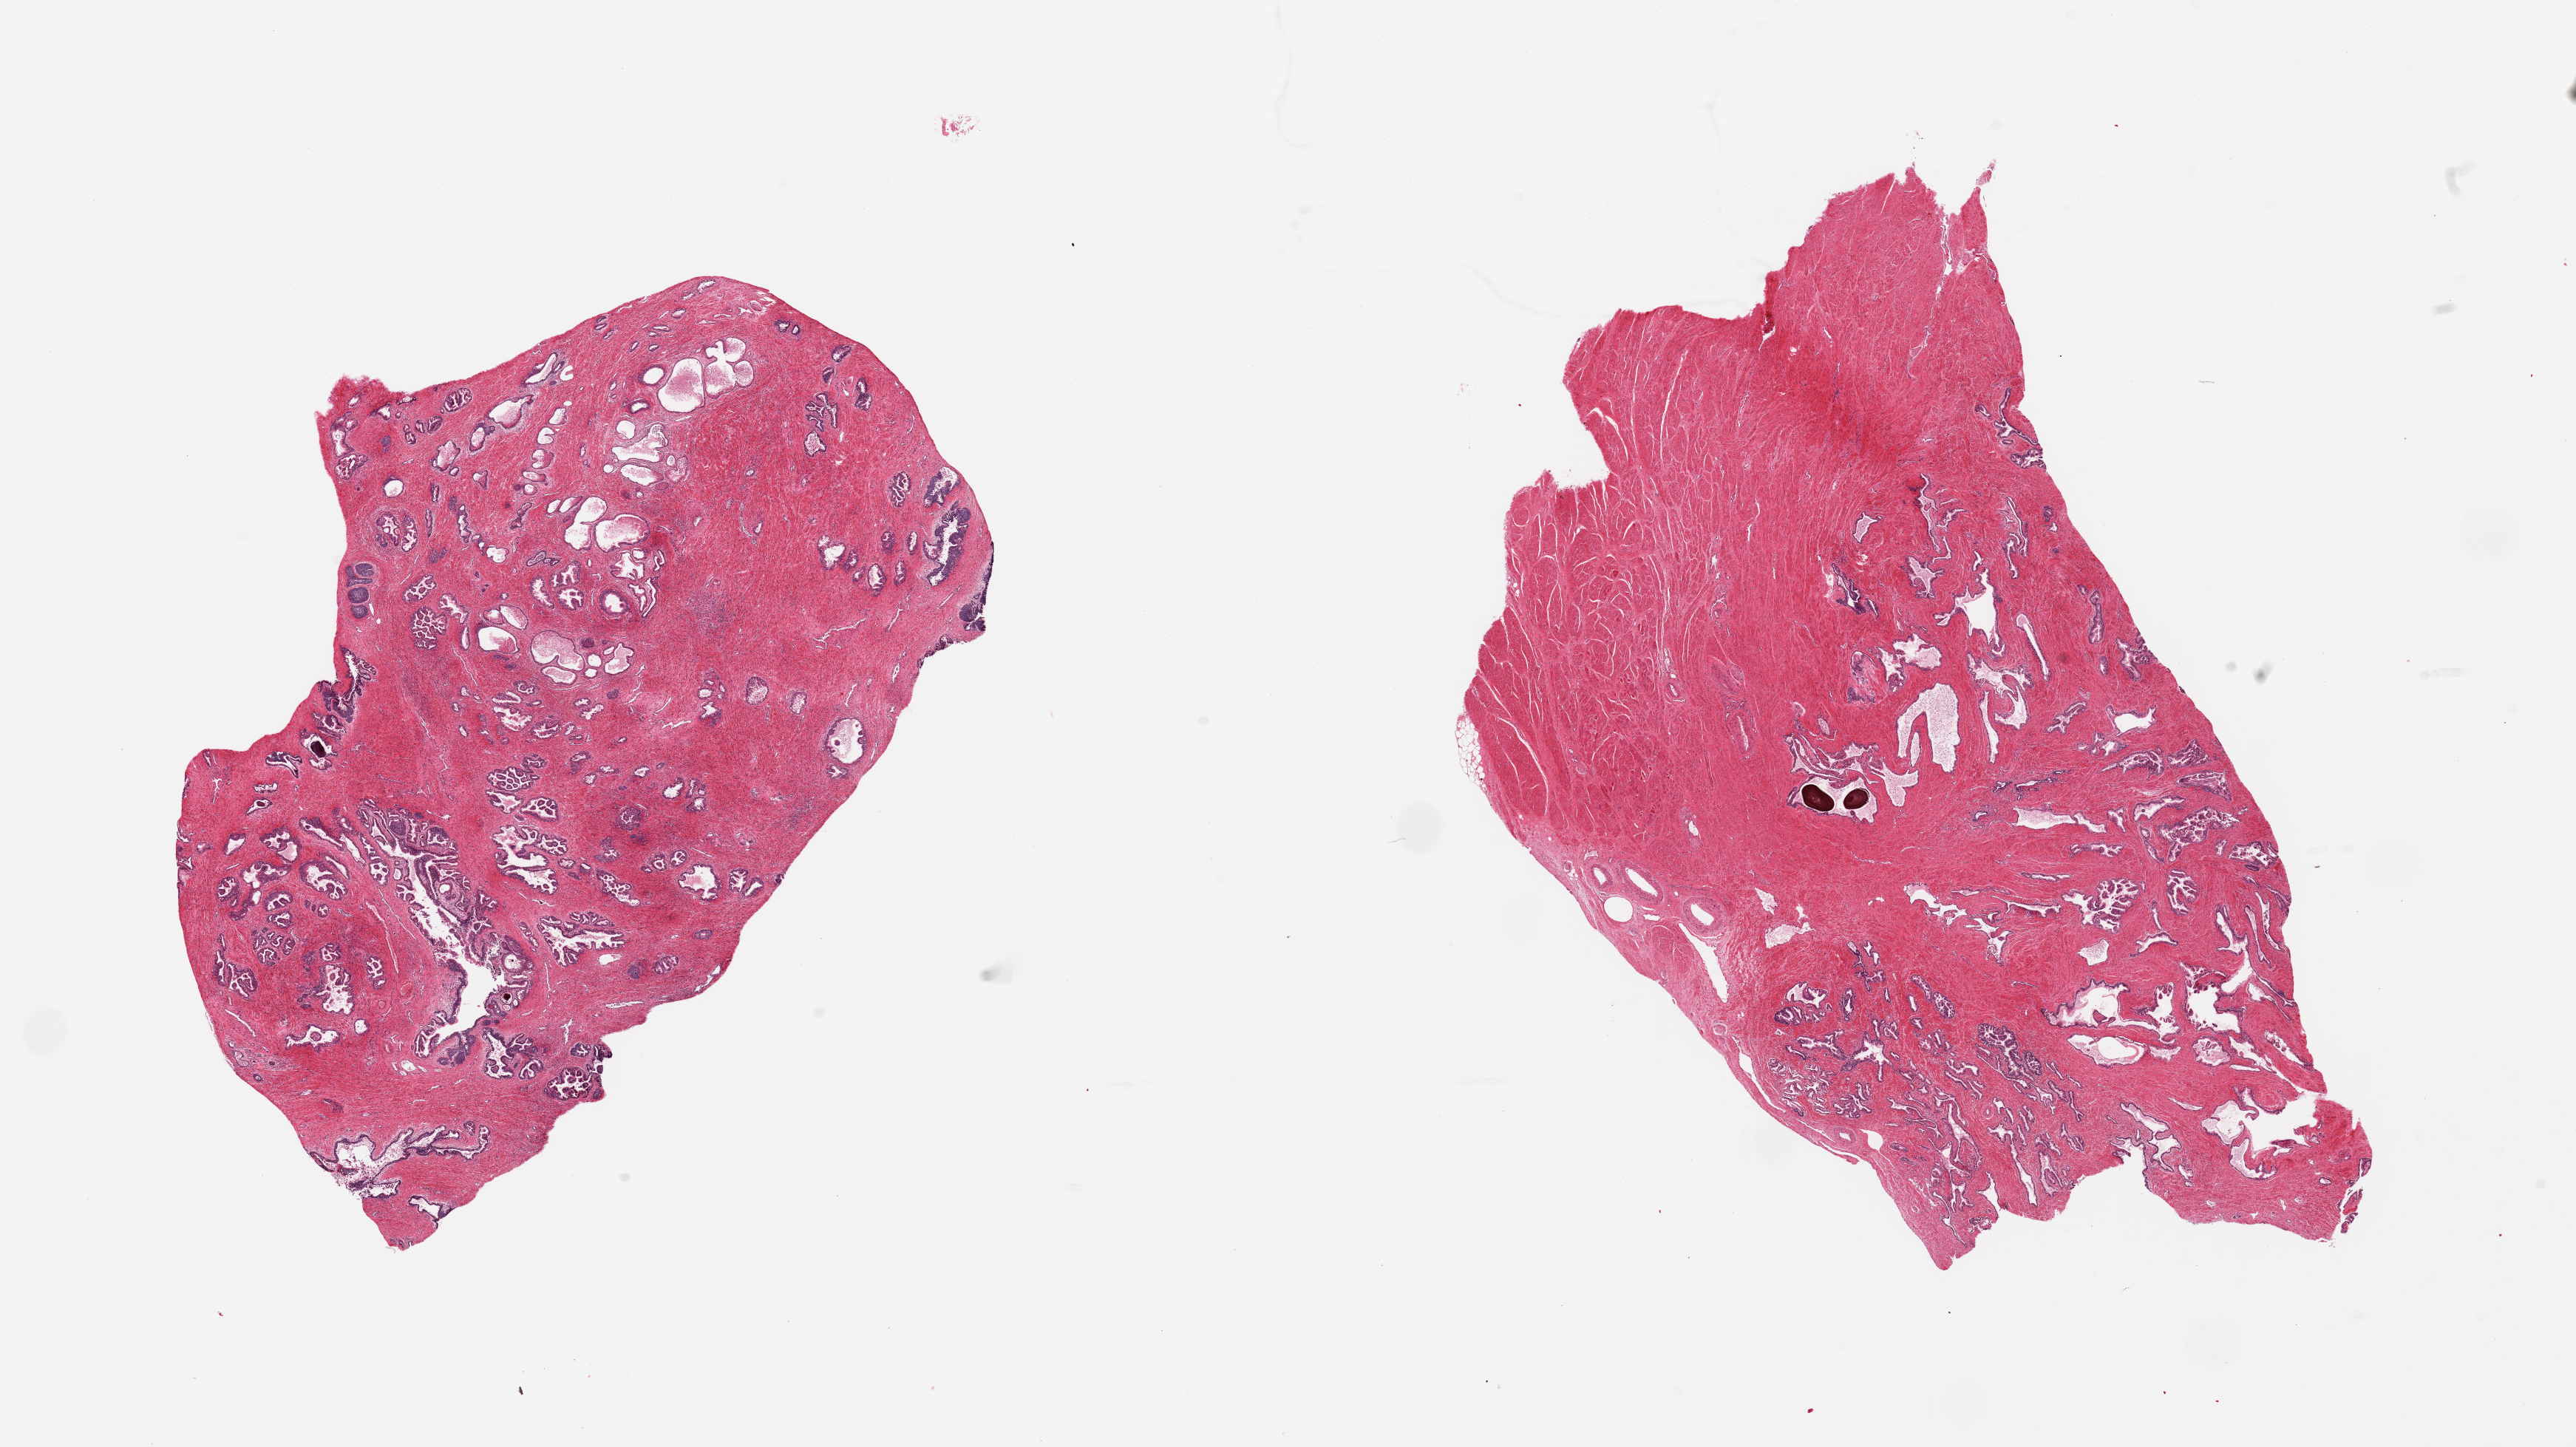
Digitized hematoxylin and eosin (H&E)-stained section, shown as a low-resolution overview of the whole scanned area (about 27.6 x 15.5 mm); PAXgene-fixed paraffin-embedded (PFPE) section; sampled site (target tissue): prostate; tissue donor sample. Donor sex: male.
Review note (as recorded): 2 pieces.